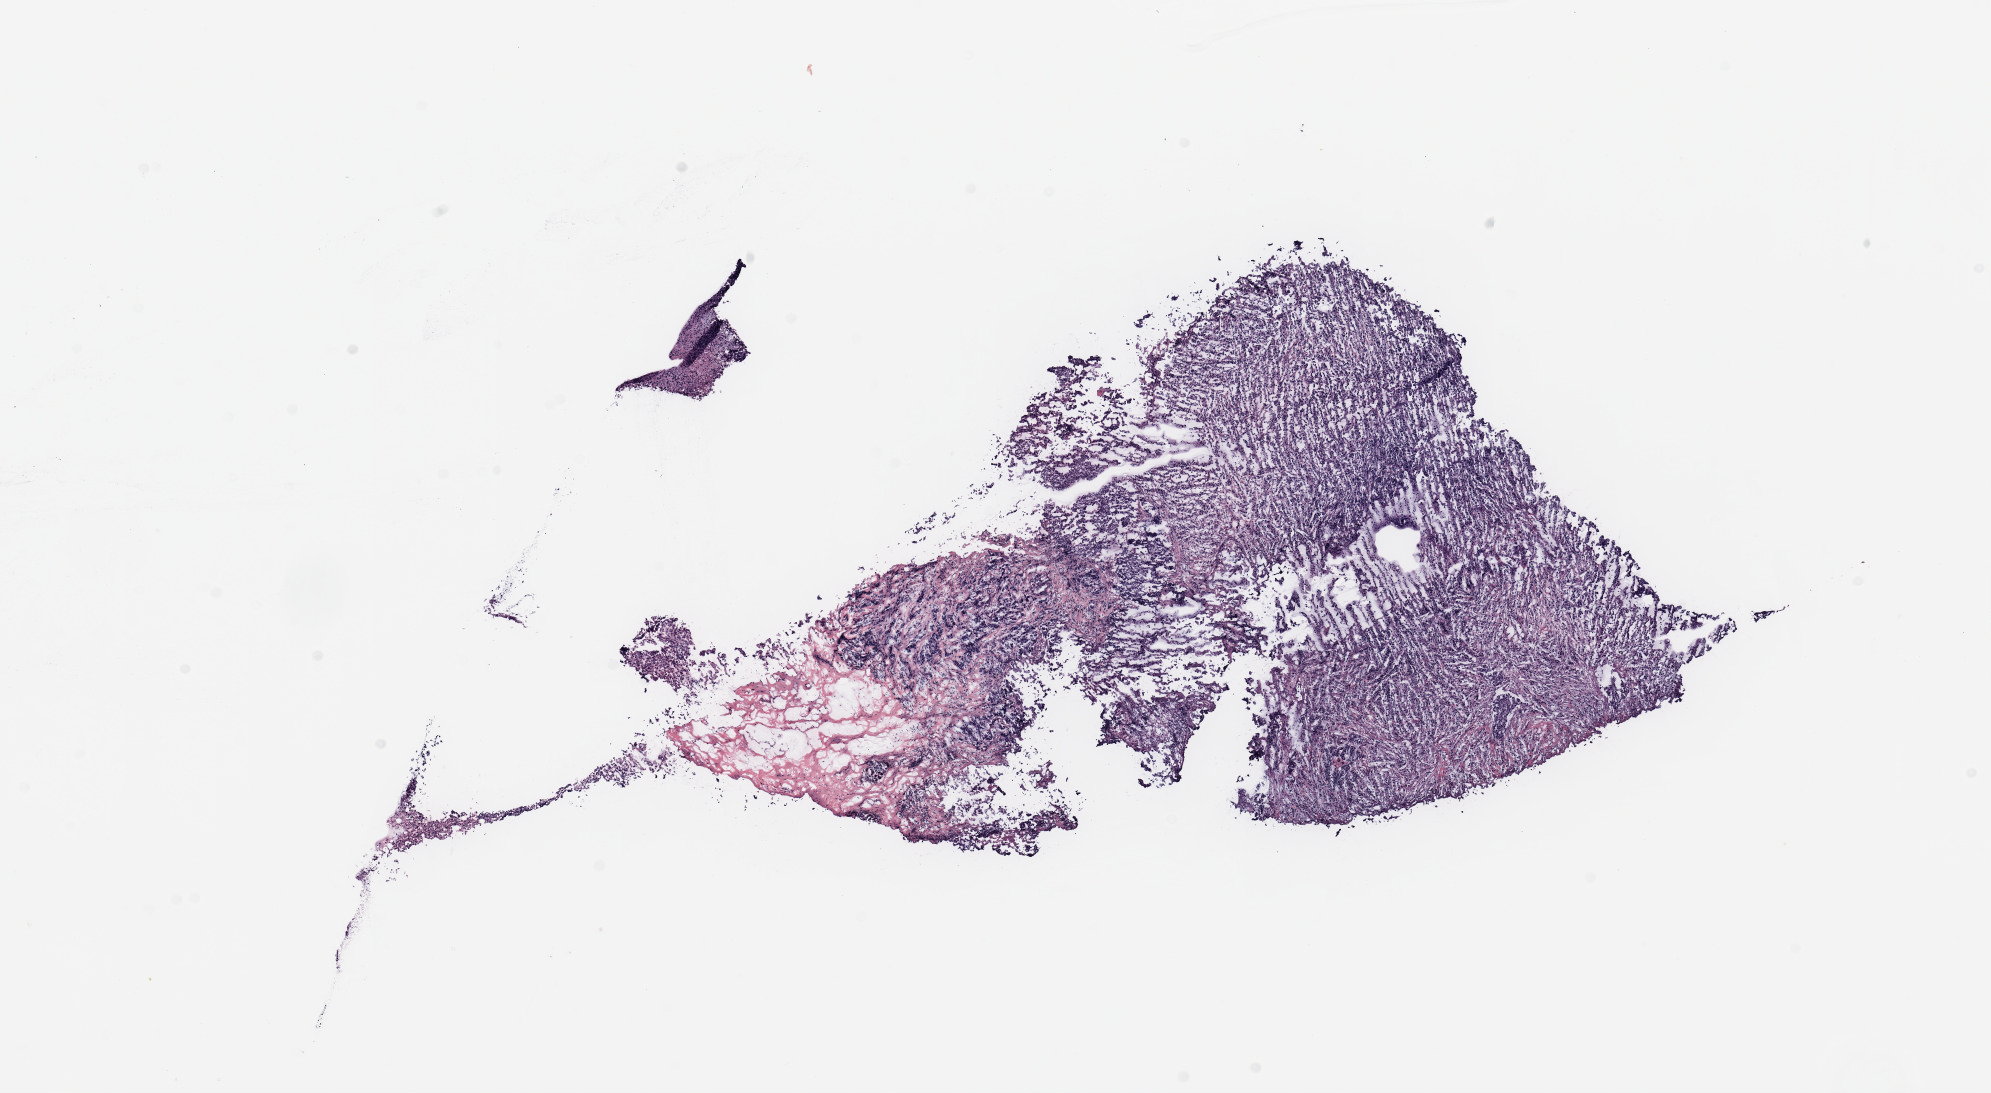
Digitized Hematoxylin and eosin (H&E) stained tissue section (whole slide), a low-resolution overview of the entire scanned area, about 15.8 x 8.6 mm (from a 20x scan), tumour tissue sample, breast. Female, 50 y/o.
- diagnosis: Infiltrating duct carcinoma, NOS
- AJCC pathologic stage: IIB